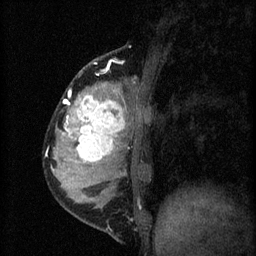
Breast MRI (dynamic contrast-enhanced), one sagittal slice. Slice 17 of 60 in the series (ordered by position). 3 images stored at this slice position (order not interpretable as contrast timing). 1.5 T. TE 4.2 ms, TR 8.2 ms. 256 × 256 image matrix. Patient: female, 37 years.
Structures marked on this image (semi-automatic segmentation, software-assisted and operator-edited):
- analysis volume of interest (the breast-tissue region the enhancement analysis was run in; not a lesion): box from (x=53, y=78) to (x=140, y=181) px
- tumour enhancement mask (voxels above the 70 % enhancement threshold inside the analysis volume of interest): (x=63, y=90)–(x=125, y=163)